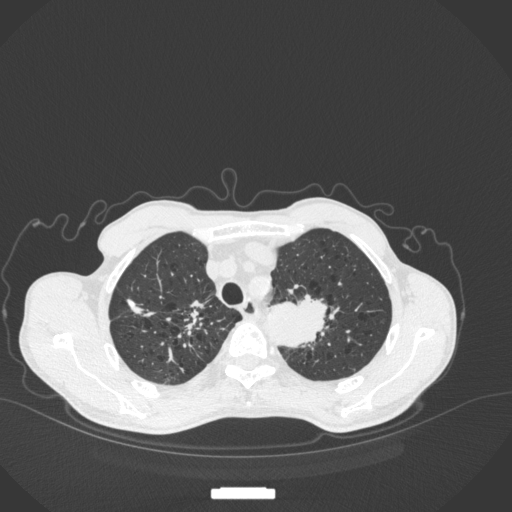
Chest CT, one axial slice; position 347 of 394 along the scan axis; reconstruction kernel B31f; 120 kVp; lung window (W 1500 / L -600 HU); 1 mm slice thickness; 512 × 512 image matrix, field of view 400 × 400 mm. Patient: male, 65 years. From the clinical record (not read from this slice): clinical TNM (as recorded): T2b N0 M0.
Annotated regions visible in this slice (rectangle marked by the reading radiologist):
- lung tumour (recorded histology: adenocarcinoma): box from (x=264, y=287) to (x=328, y=353) px